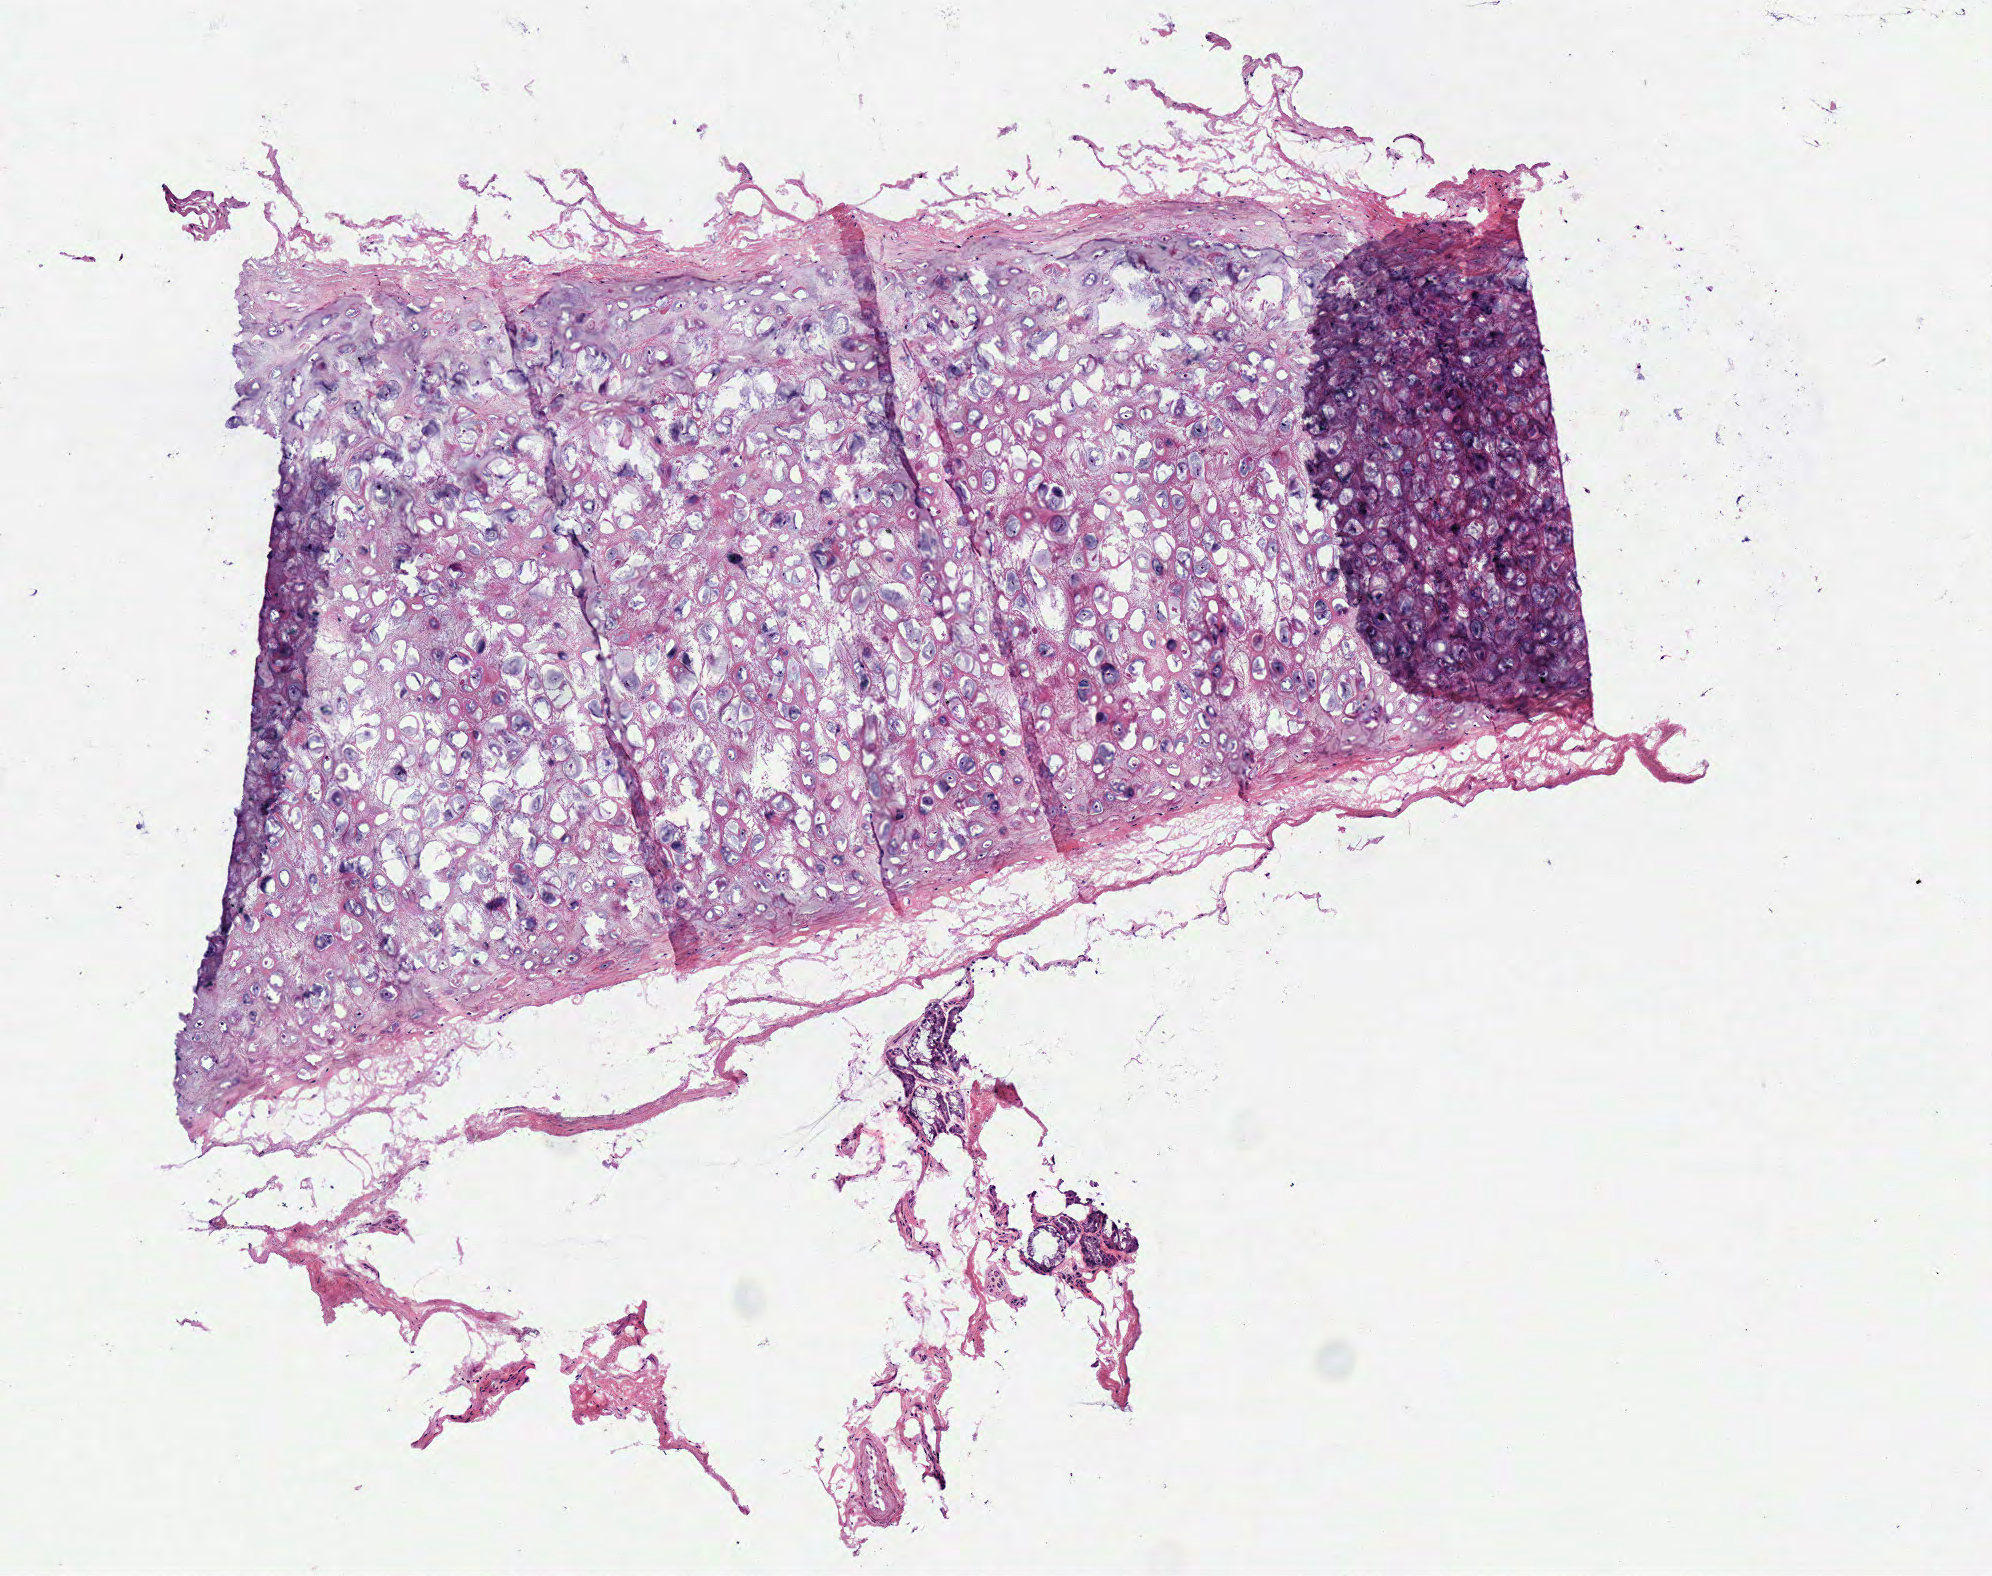
Whole-slide histology image, Hematoxylin and eosin (H&E) stained, shown as a low-resolution overview of the whole scanned area (about 3.9 x 3.1 mm); frozen section; solid tissue normal (non-tumour tissue) sample from the head and neck. Male patient; age at initial diagnosis 80 years.
* this section: solid tissue normal sample (biorepository sample class)
* patient diagnosis: Squamous cell carcinoma, NOS (larynx, NOS)